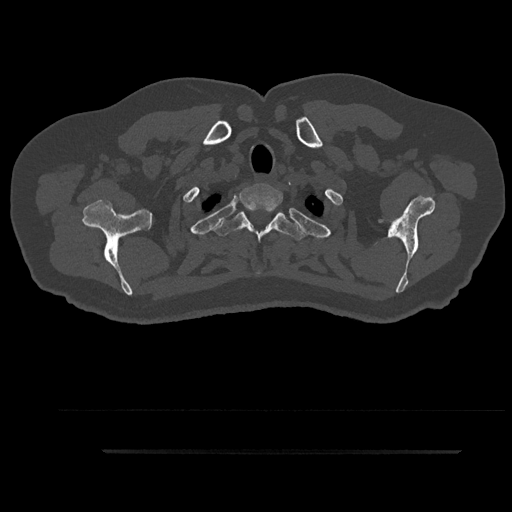
CT including the spine, one axial slice; reconstruction kernel Br40s/3; 120 kVp; bone window (W 1800 / L 400 HU); 0.5 mm slice thickness; 512 × 512 image matrix. Male patient, age 63 years. From the clinical record (not read from this slice): primary cancer: renal; vertebrae with lytic lesions (as recorded): T8.
Structures marked on this image (semi-automatic segmentation, software-assisted and operator-edited):
- T1 vertebra: box from (x=239, y=185) to (x=283, y=212) px
- T2 vertebra: (x=213, y=209)–(x=306, y=275)